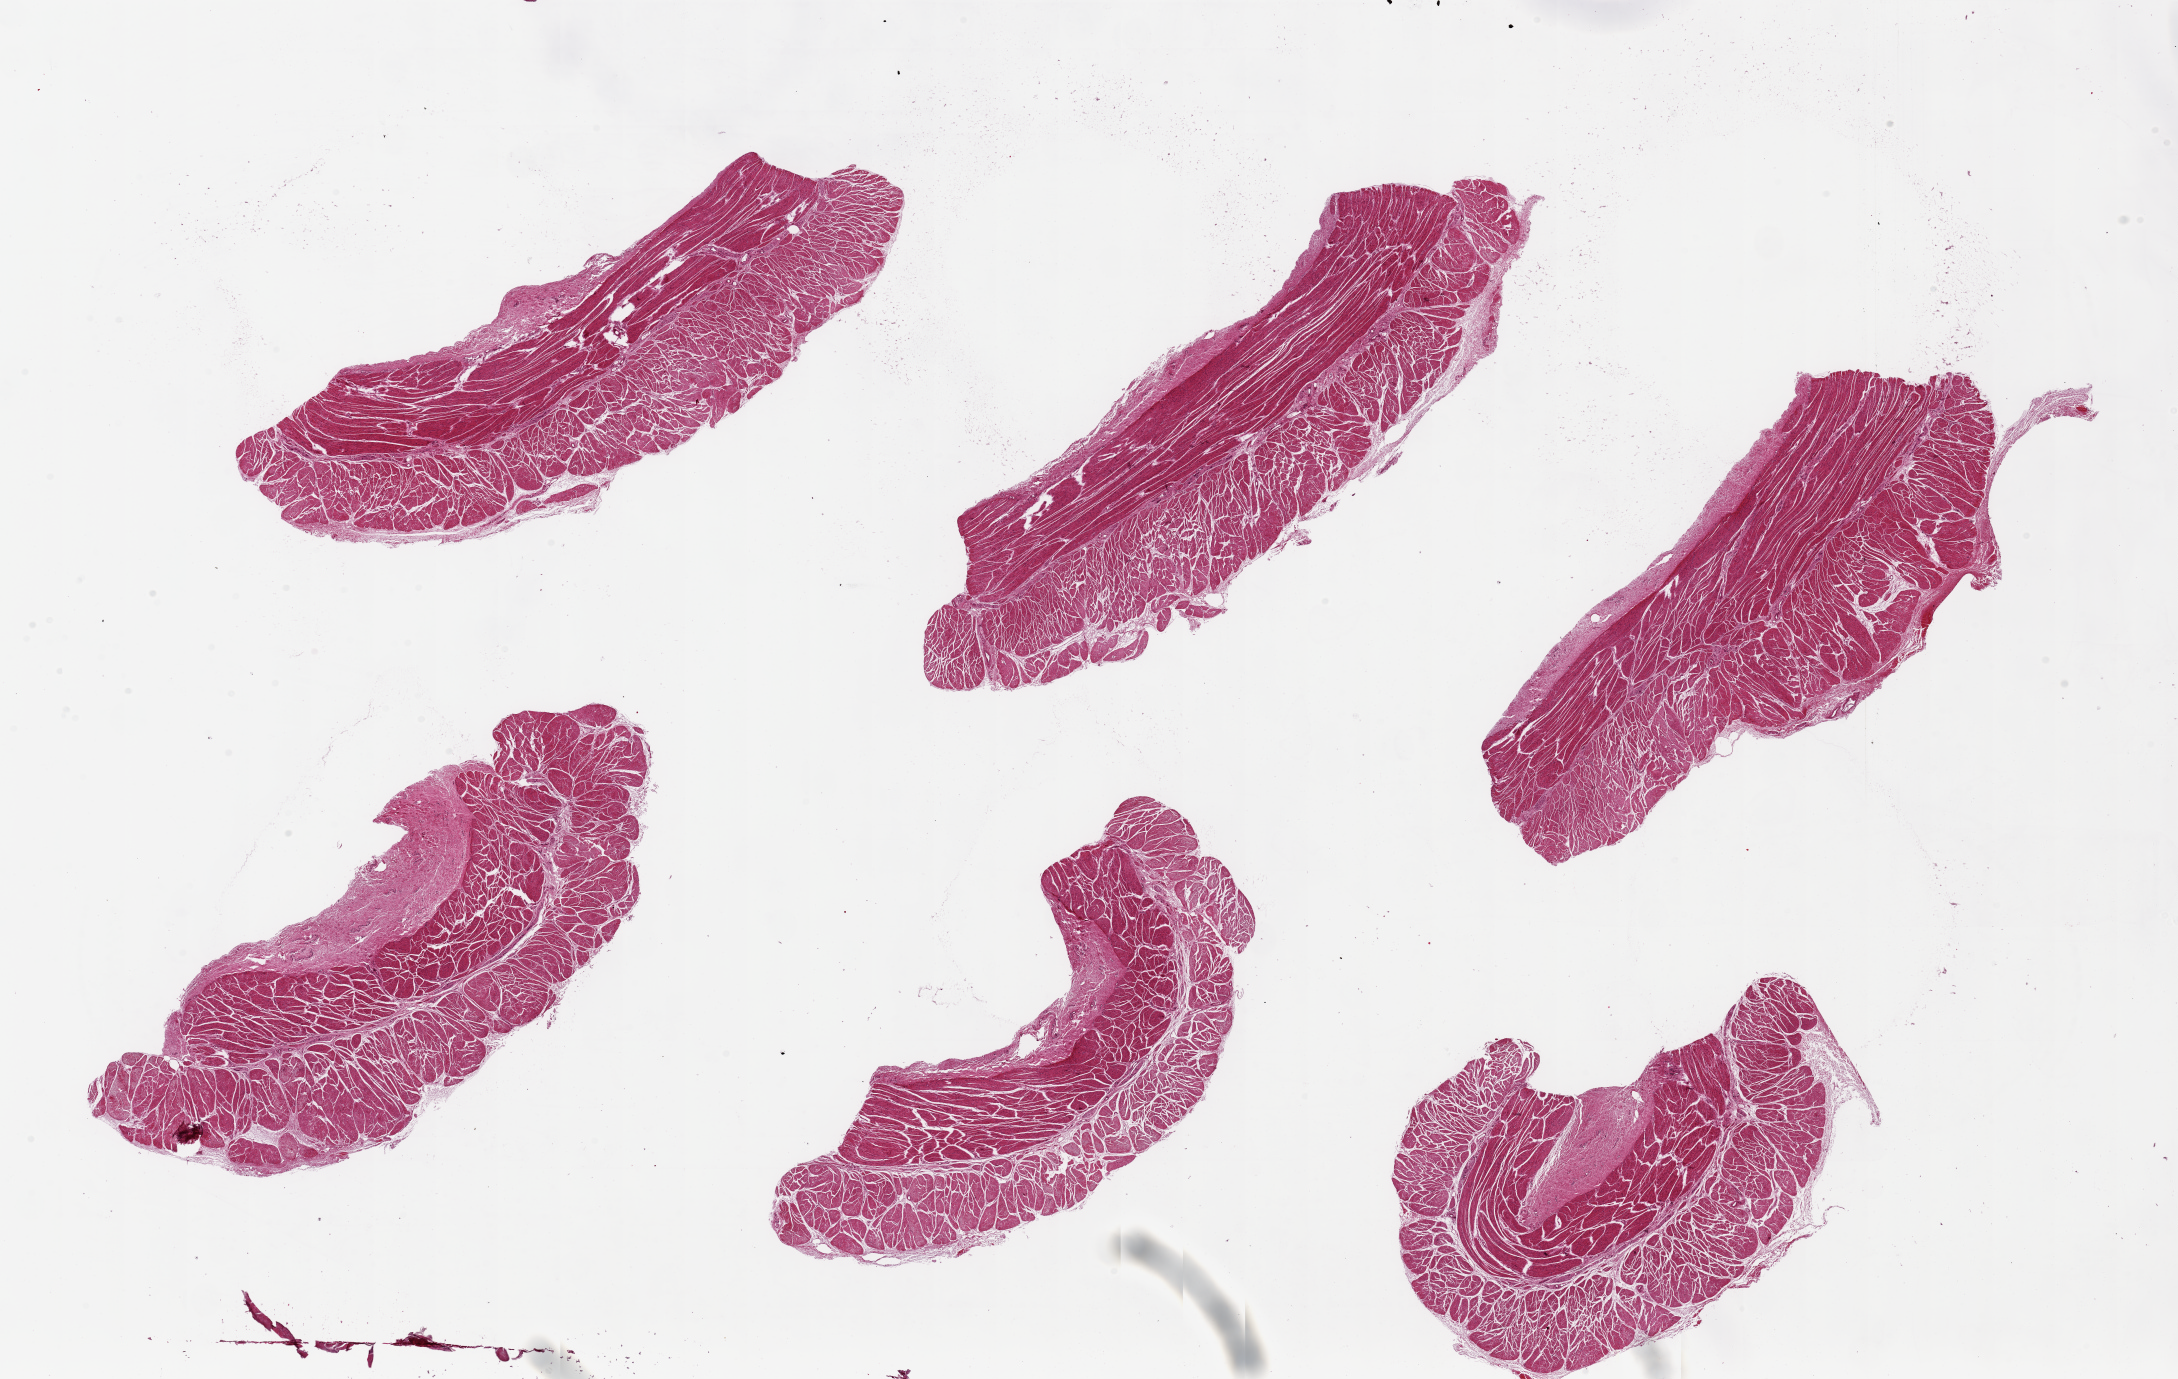
Digitized hematoxylin and eosin (H&E)-stained section, shown as a low-resolution overview of the whole scanned area (about 34.5 x 21.8 mm, slide scanned at 20x), PAXgene-fixed paraffin-embedded (PFPE) section, sampled site (target tissue): esophageal muscle, tissue donor sample. Donor: female.
Review note (as recorded): 6 pieces, up to 12x4mm; all muscularis; good specimens.